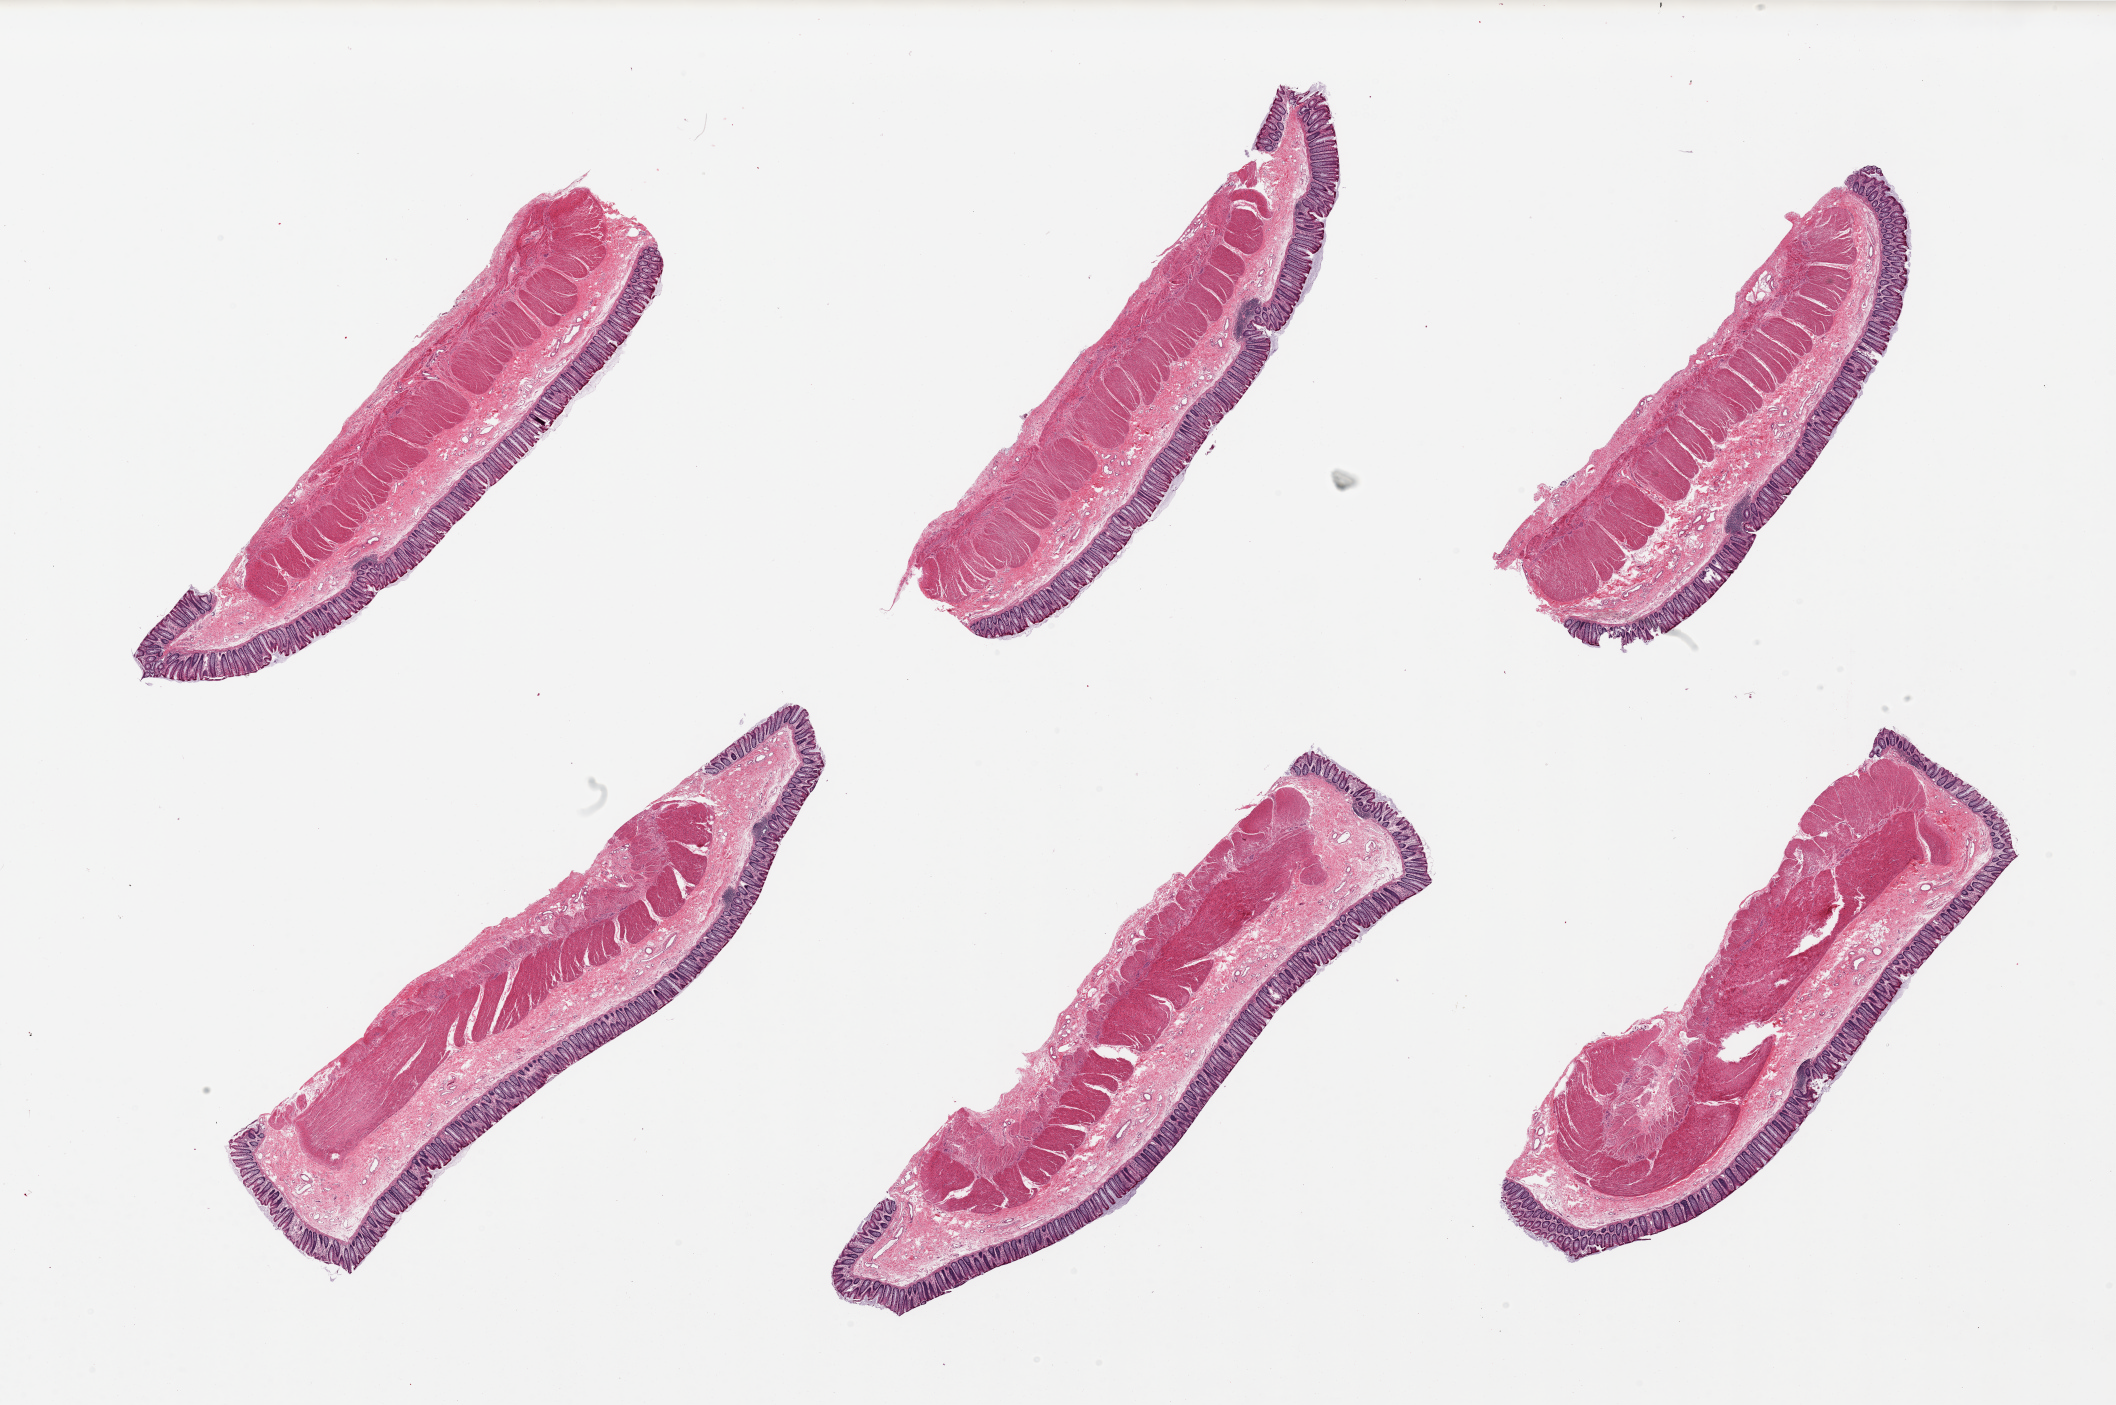
Whole-slide image, hematoxylin and eosin (H&E) stain, brightfield — shown as a low-resolution overview of the whole scanned area (about 33.5 x 22.2 mm, slide scanned at 20x), PAXgene-fixed, paraffin-embedded tissue, target tissue: transverse colon, donor tissue sample. Donor sex: female.
Pathologist's review note for this sample: 6 pieces, well preserved. Mucosa is ~15-20% thickness.